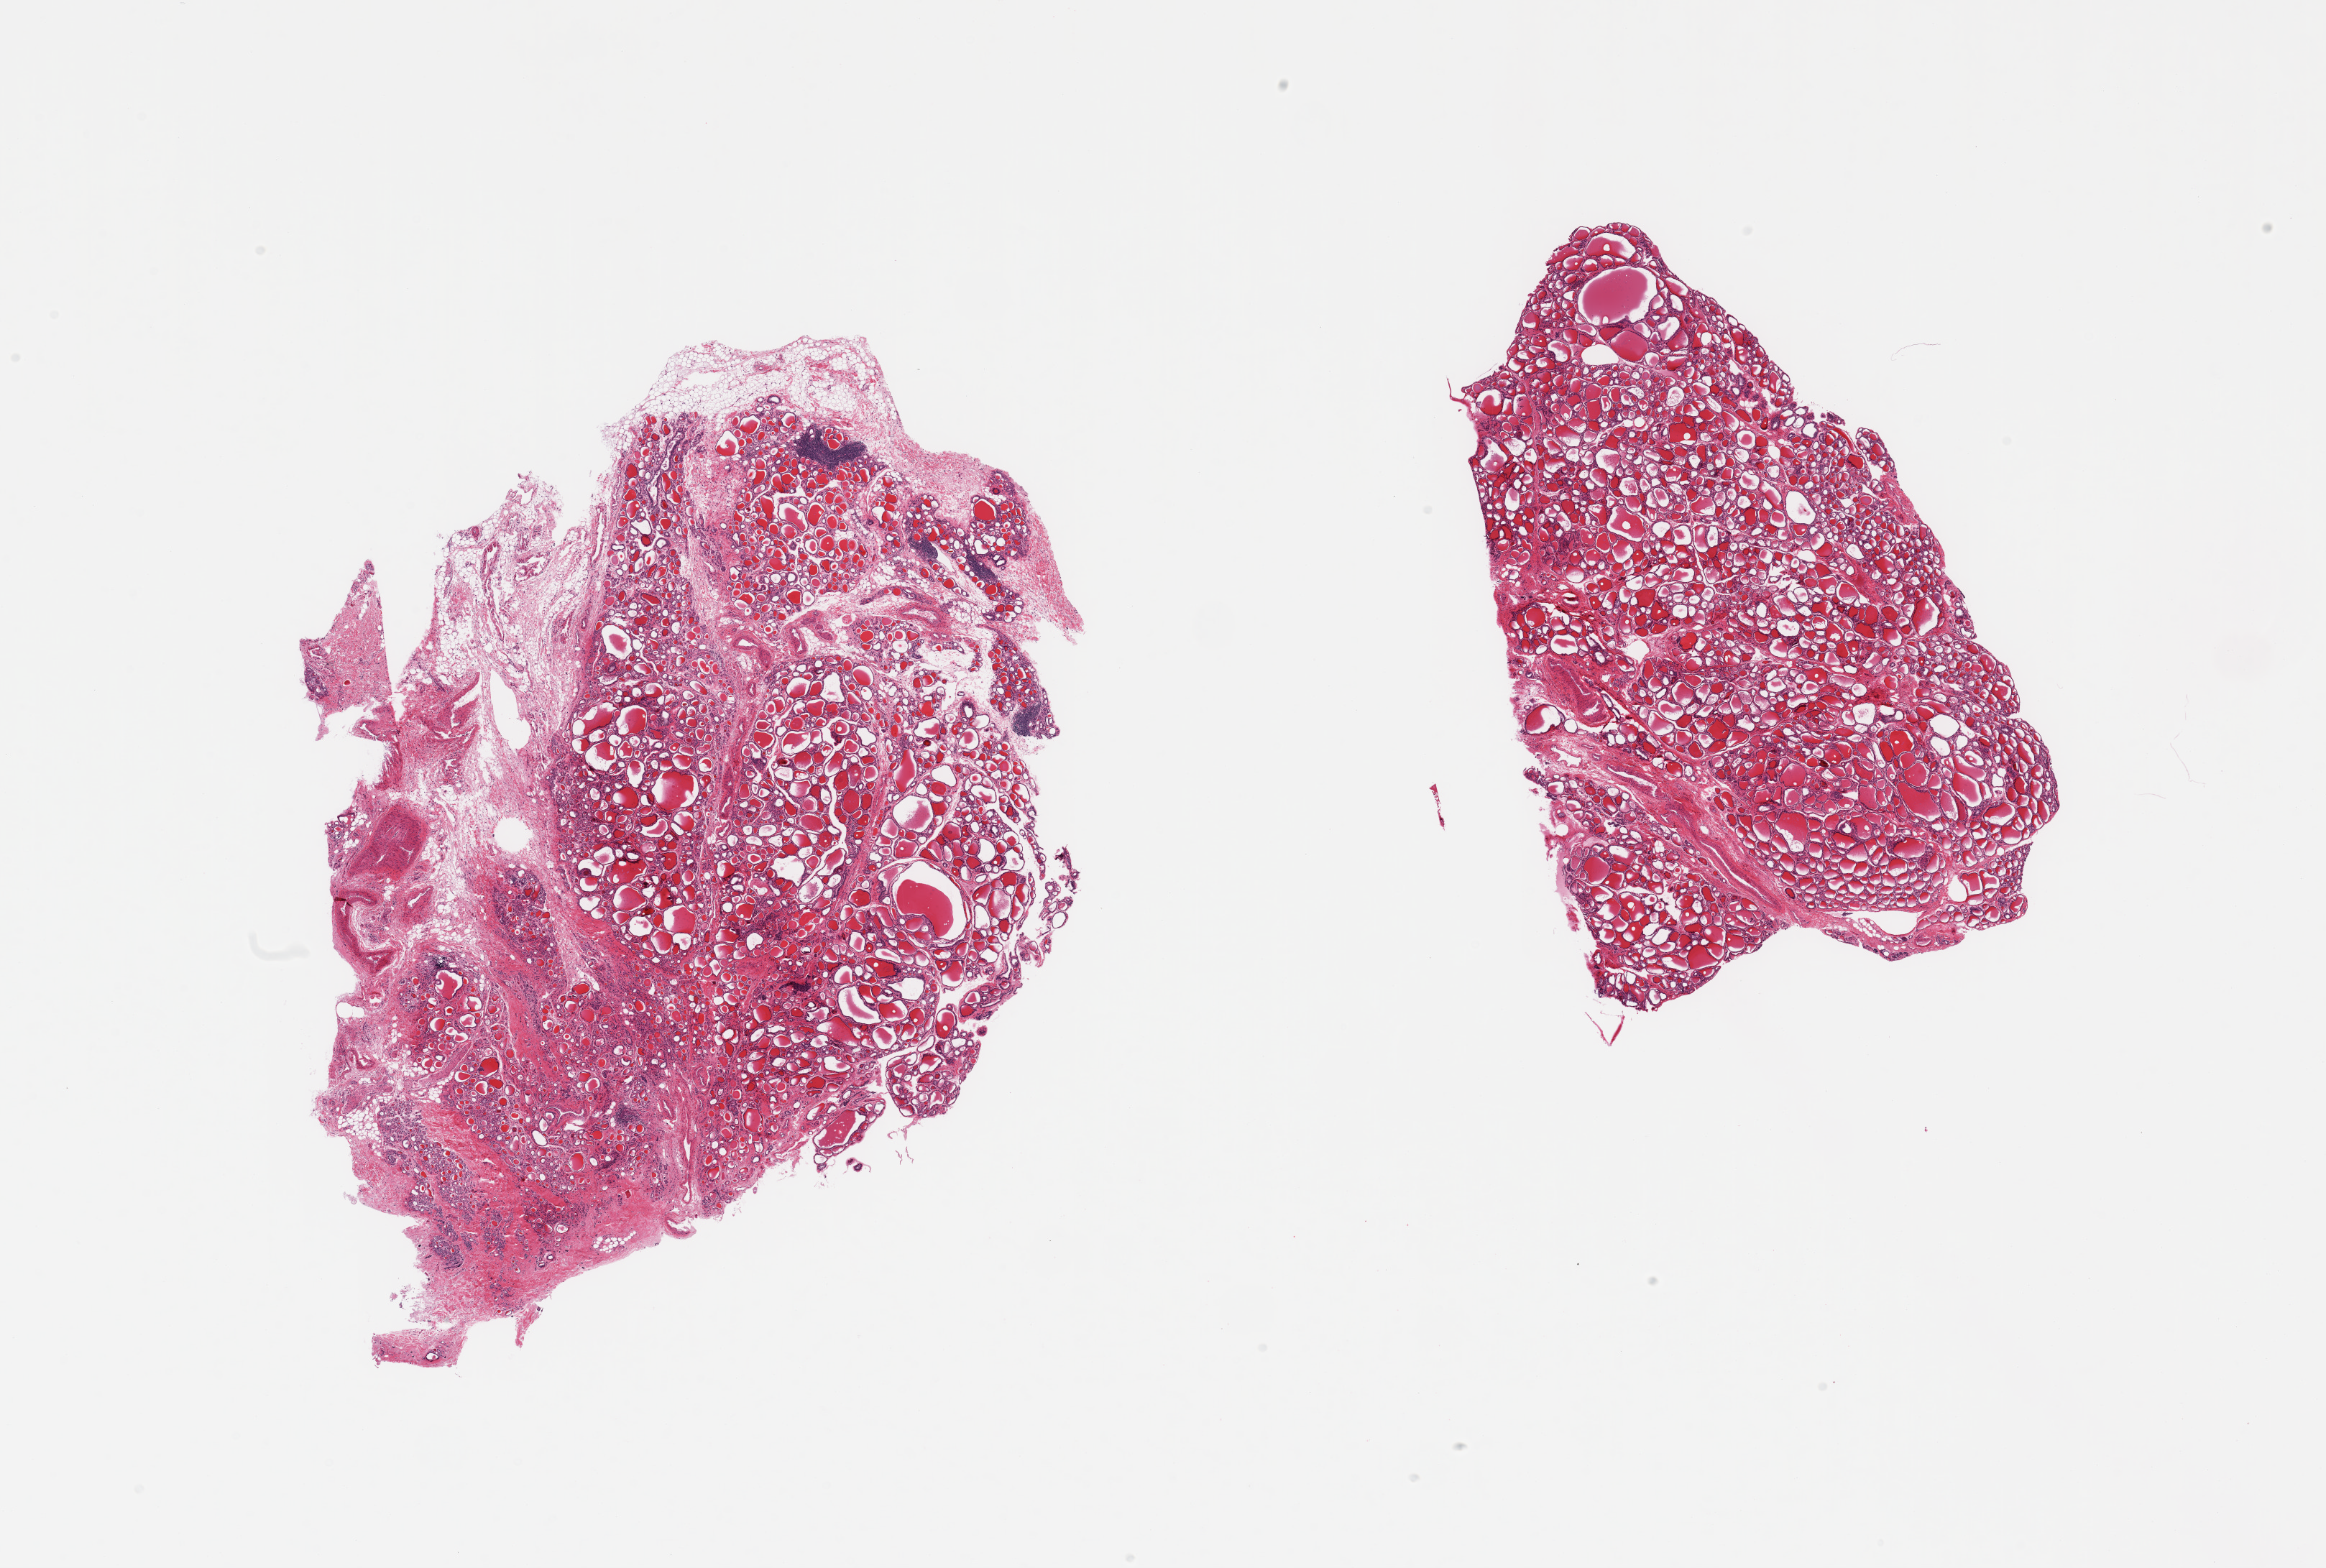
Whole-slide image, hematoxylin and eosin (H&E) stain, a low-resolution overview of the entire scanned area, about 25.6 x 17.3 mm (acquisition: 20x scan); PAXgene-fixed paraffin-embedded (PFPE) section; section of thyroid (target tissue); tissue donor sample. Donor: female.
Pathologist's review note for this sample: 2 pieces, ~15-20% adherent fat/vascular elements; nodular goitre, regressive changes.